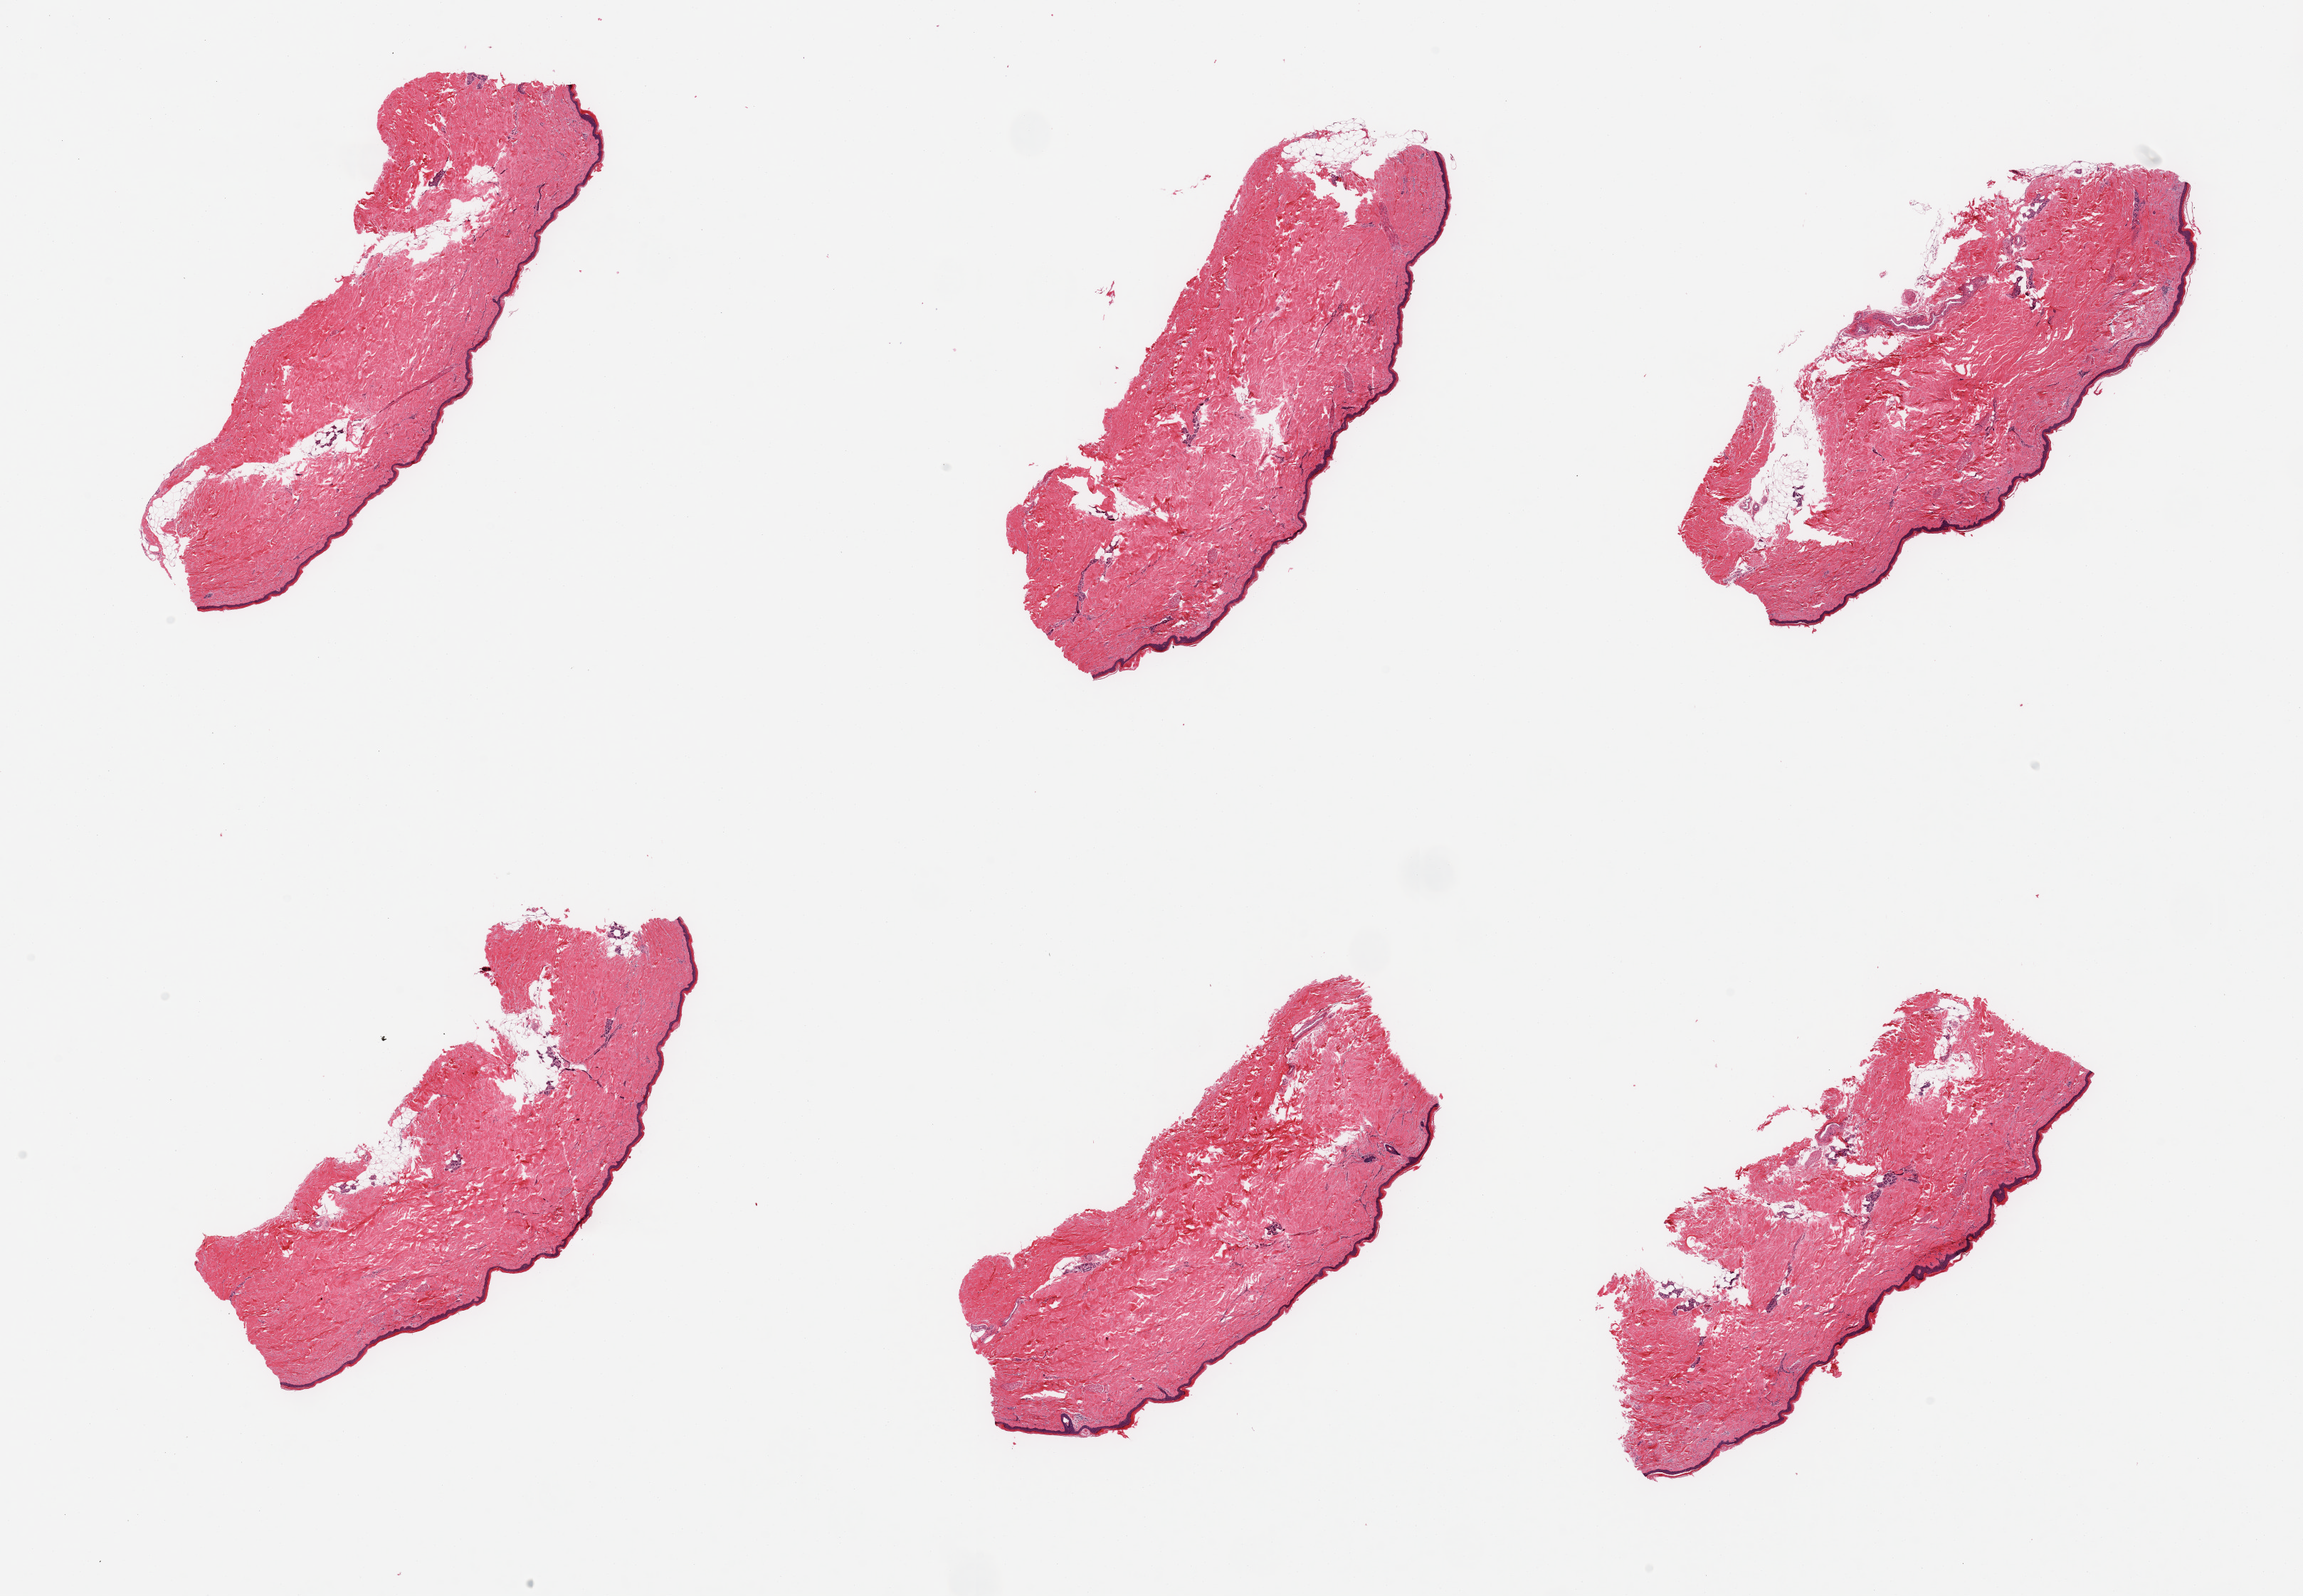
Digitized haematoxylin and eosin-stained section, brightfield — low-resolution overview of the scanned area, about 25.6 x 17.7 mm (acquisition: 20x scan); PAXgene-fixed paraffin-embedded (PFPE) section; target tissue: skin of lower leg; tissue donor sample. Donor: female.
- review note (as recorded): 6 pieces; well trimmed; 10% dermal fat